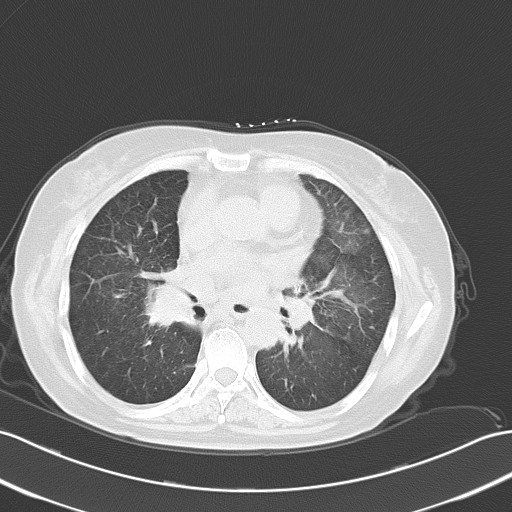
Chest CT, one axial slice. Slice 34 of 62 in the series (ordered by position). Reconstruction kernel B70f. Lung window (W 1500 / L -600 HU). 512 × 512 image matrix. Female patient, age 65 years. From the clinical record (not read from this slice): clinical TNM (as recorded): T1c N3 M0; histopathological grade: G3.
Structures marked on this image (rectangle marked by the reading radiologist):
- lung tumour (recorded histology: small cell carcinoma): bounding box (x1, y1, x2, y2) in pixels: (142, 276, 207, 342)